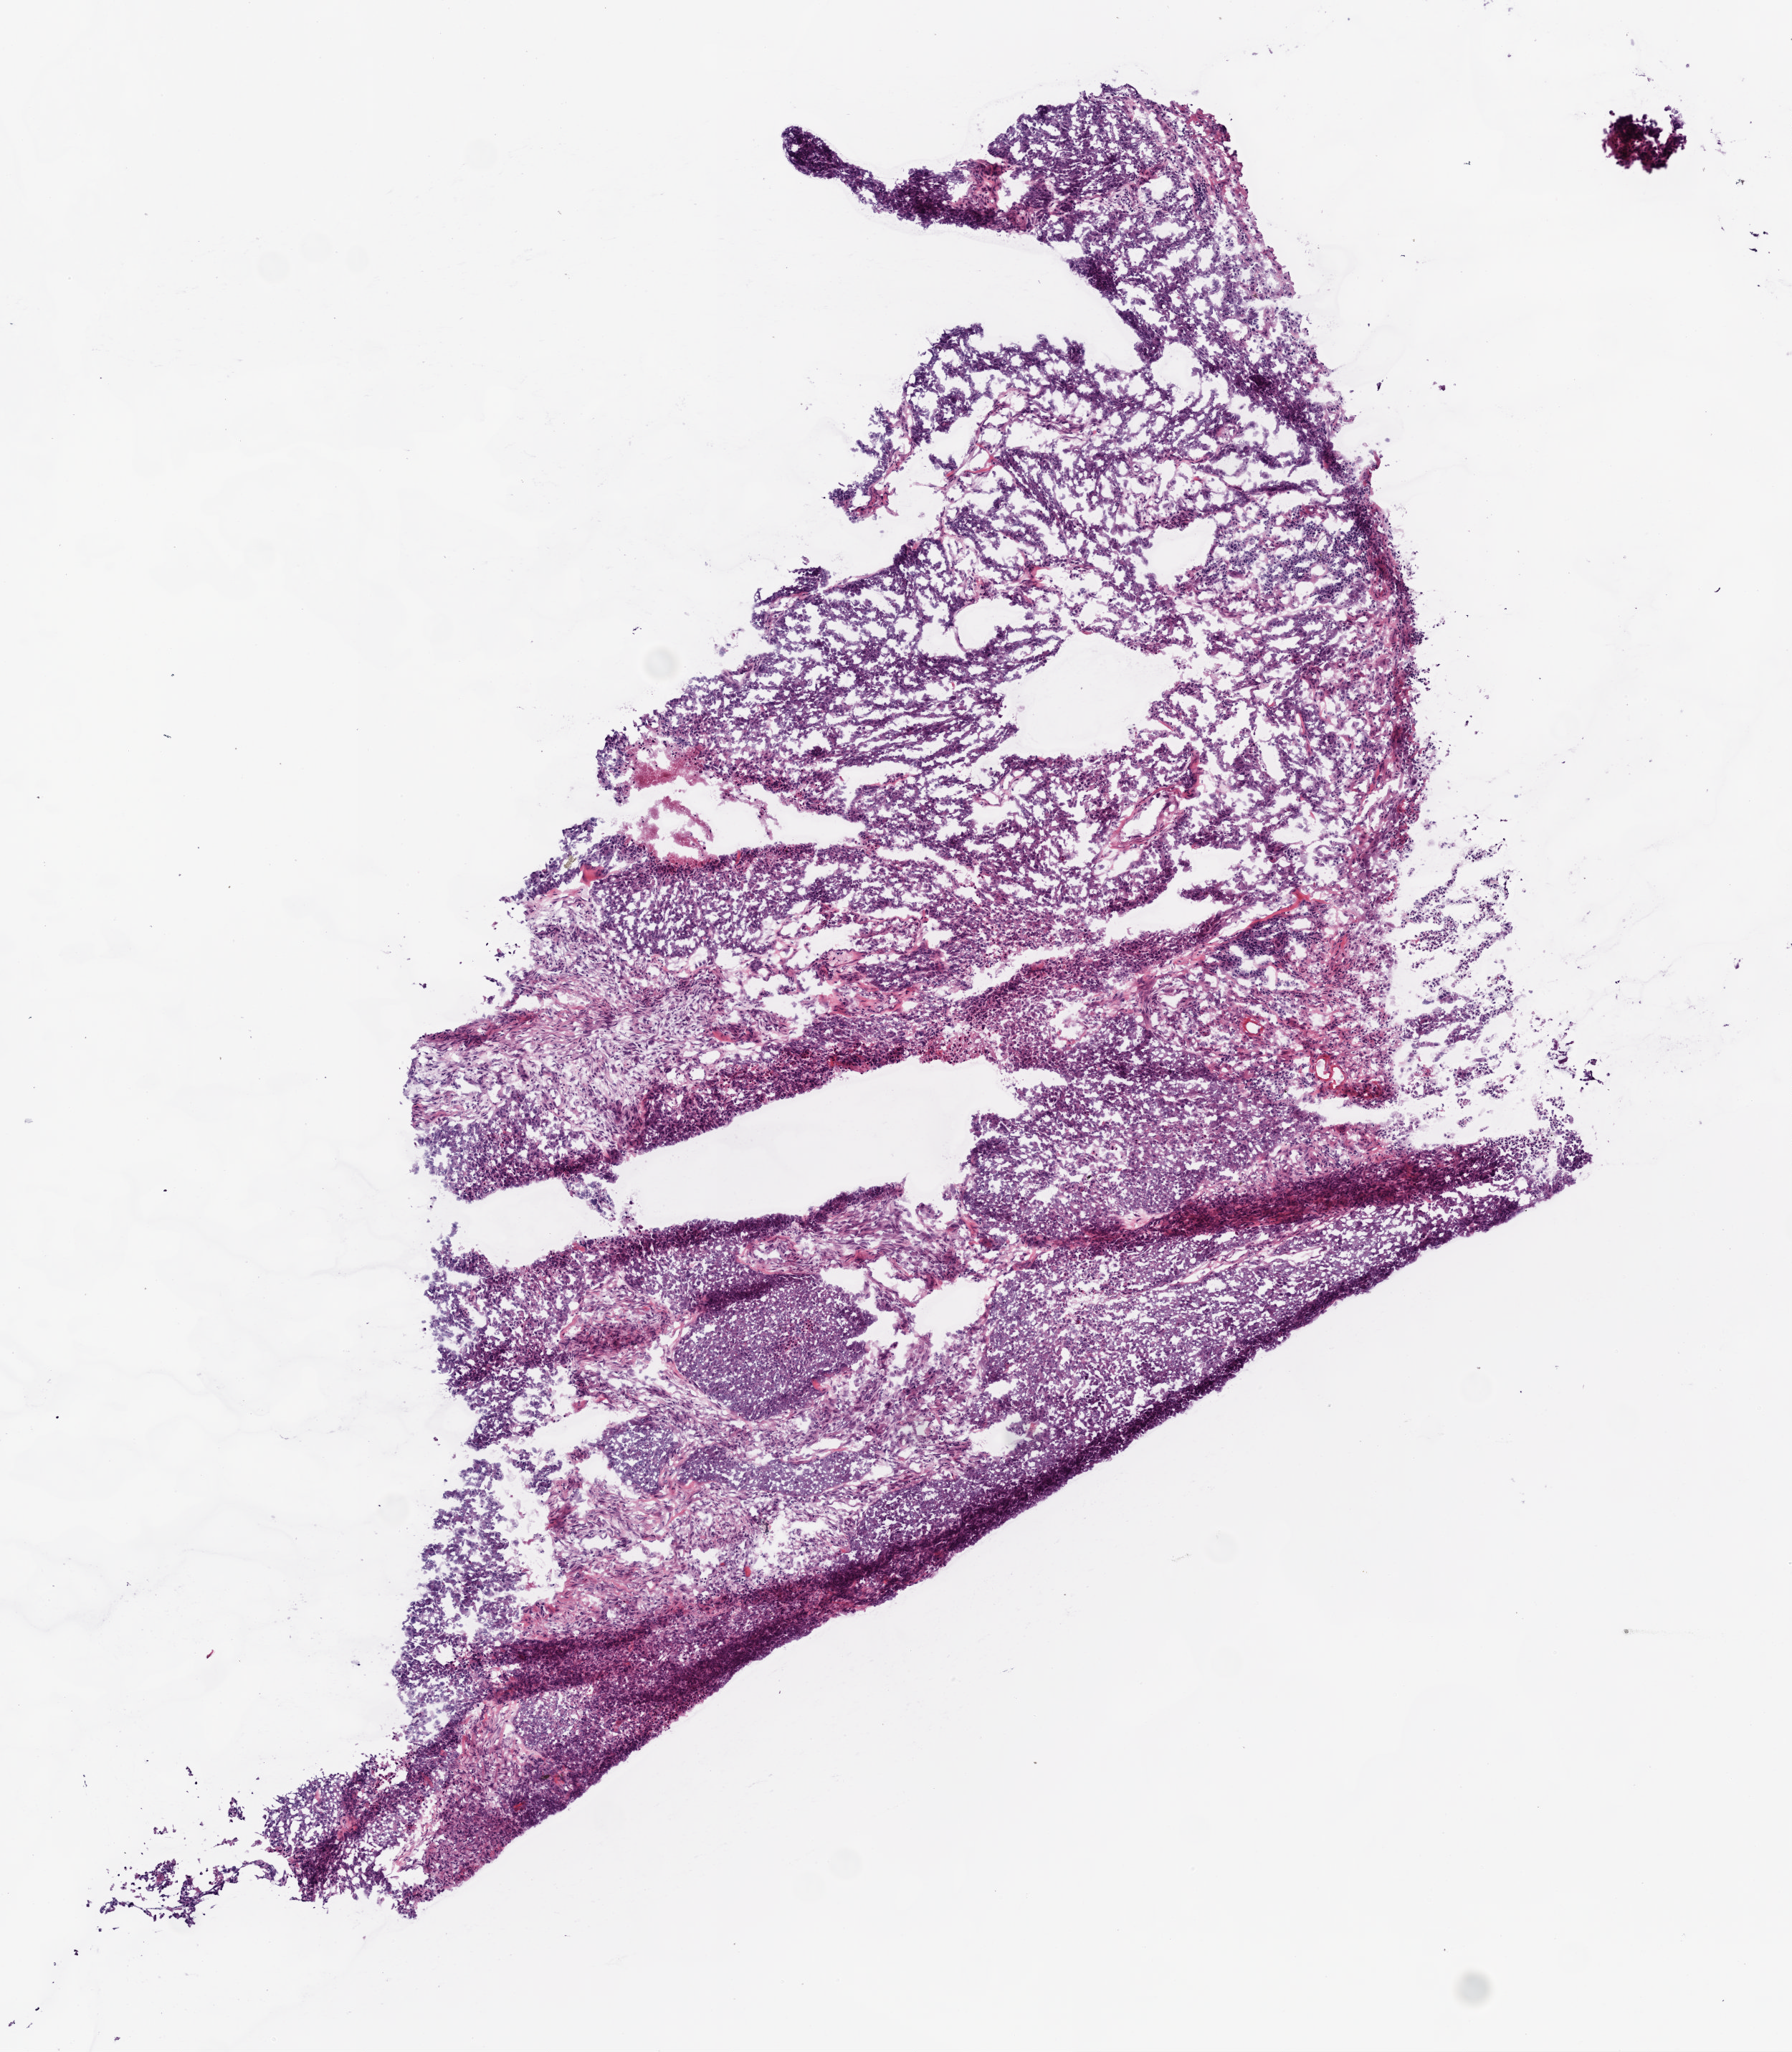
Digitized Hematoxylin and eosin (H&E) stained tissue section (whole slide), a low-resolution overview of the entire scanned area, about 5.0 x 5.7 mm (slide scanned at 20x). Frozen section from the bottom of the tissue portion. Ovary, primary tumour sample. Patient: female, age at initial diagnosis 65 years. Histologic grade: G3 (poorly differentiated). Pathologist review of this section (percent, as recorded): tumour cells 94%, tumour nuclei 95%, normal cells 0%, stromal cells 5%, necrosis 1%.
FIGO stage: IIIC. Diagnosis: Serous cystadenocarcinoma, NOS.